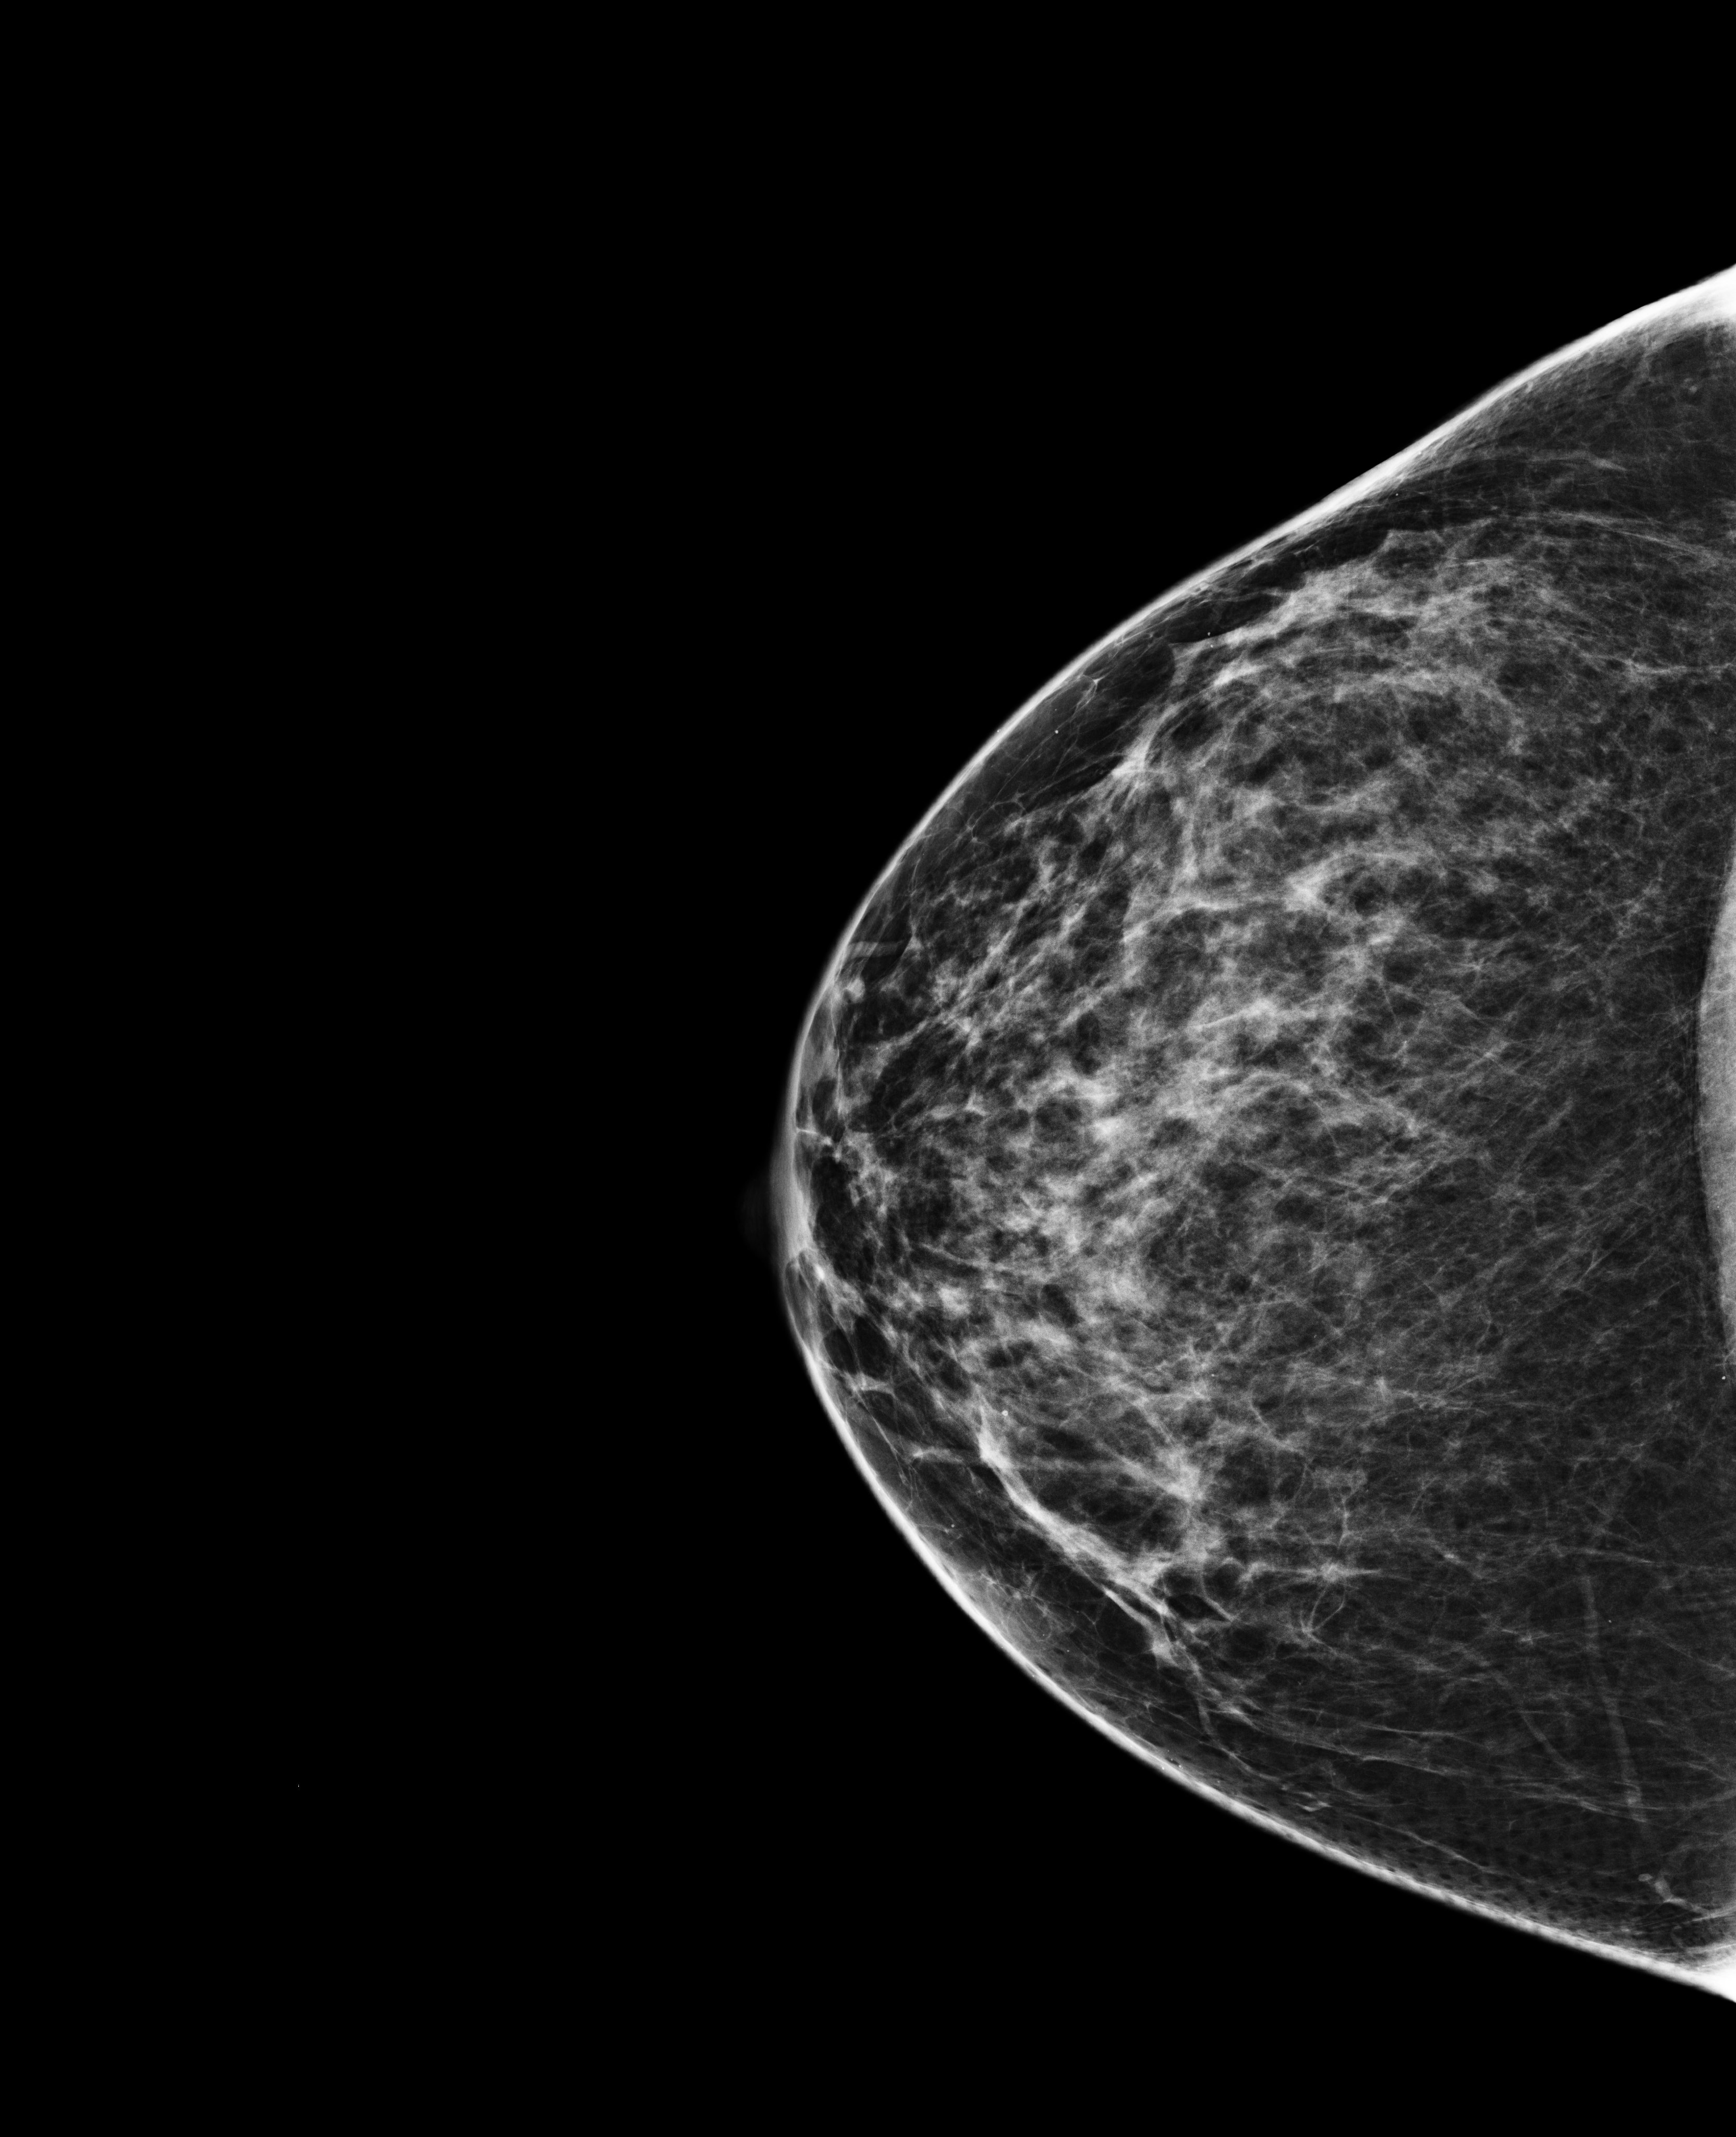
Full-field digital mammogram (FFDM), right breast, cranio-caudal projection, screening examination, compressed breast thickness 61 mm. Patient: female, 47 years.
BI-RADS breast density category at the screening exam (both breasts, scale 1–4): 3. Final BI-RADS assessment for this screening round (tomosynthesis exam, both breasts): category 1. Recall: no recall after this screen.